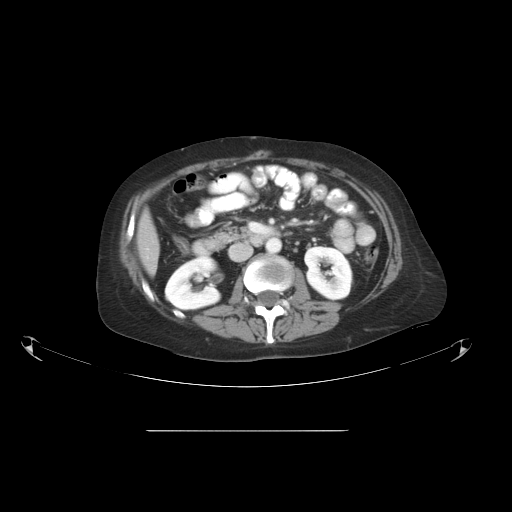
Contrast-enhanced abdominal CT, one axial slice; position 21 of 51 along the scan axis; reconstruction kernel STANDARD; intravenous contrast given; soft-tissue window (W 400 / L 40 HU); 512 × 512 image matrix, field of view 475 × 475 mm. Female patient, age 48 years. Case-level facts recorded for this patient, not image findings: diagnosis: colorectal cancer liver metastases, imaged before liver resection.
Outlined on this slice (expert manual segmentation):
- liver: bounding box (x1, y1, x2, y2) in pixels: (139, 214, 159, 274)
- planned liver remnant (the part of the liver to remain after resection): (139, 213, 159, 274)